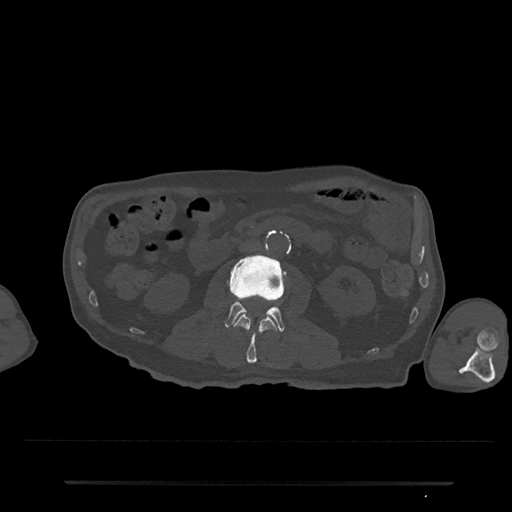
CT including the spine, one axial slice; slice 21 of 797 in the series (ordered by position); bone window (W 1800 / L 400 HU); 0.5 mm slice thickness; 512 × 512 image matrix, field of view 427 × 427 mm. Patient: male, 74 years. From the clinical record (not read from this slice): primary cancer: prostate.
Outlined on this slice (semi-automatic segmentation, software-assisted and operator-edited):
- L2 vertebra: bounding box [x1, y1, x2, y2] px = [234, 314, 277, 364]
- L3 vertebra: [214, 255, 286, 332]